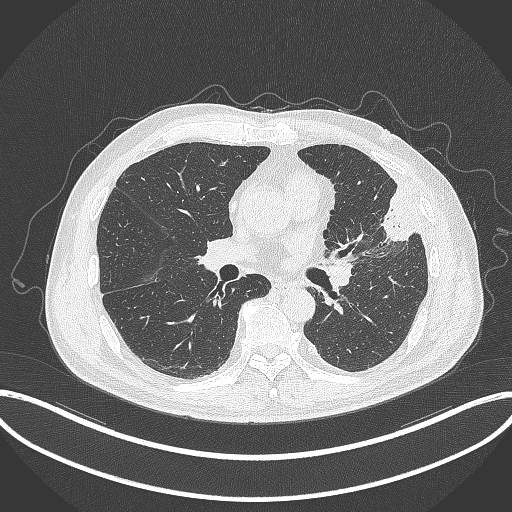
Chest CT, one axial slice. Slice 174 of 382 in the series (ordered by position). Reconstruction kernel B70f. 120 kVp. Lung window (W 1500 / L -600 HU). 512 × 512 image matrix. Male patient, age 64 years. From the clinical record (not read from this slice): clinical TNM (as recorded): T4 N1 M0; histopathological grade: G3.
Structures marked on this image (rectangle marked by the reading radiologist):
- lung tumour (recorded histology: adenocarcinoma): bounding box (x1, y1, x2, y2) in pixels: (372, 183, 424, 246)